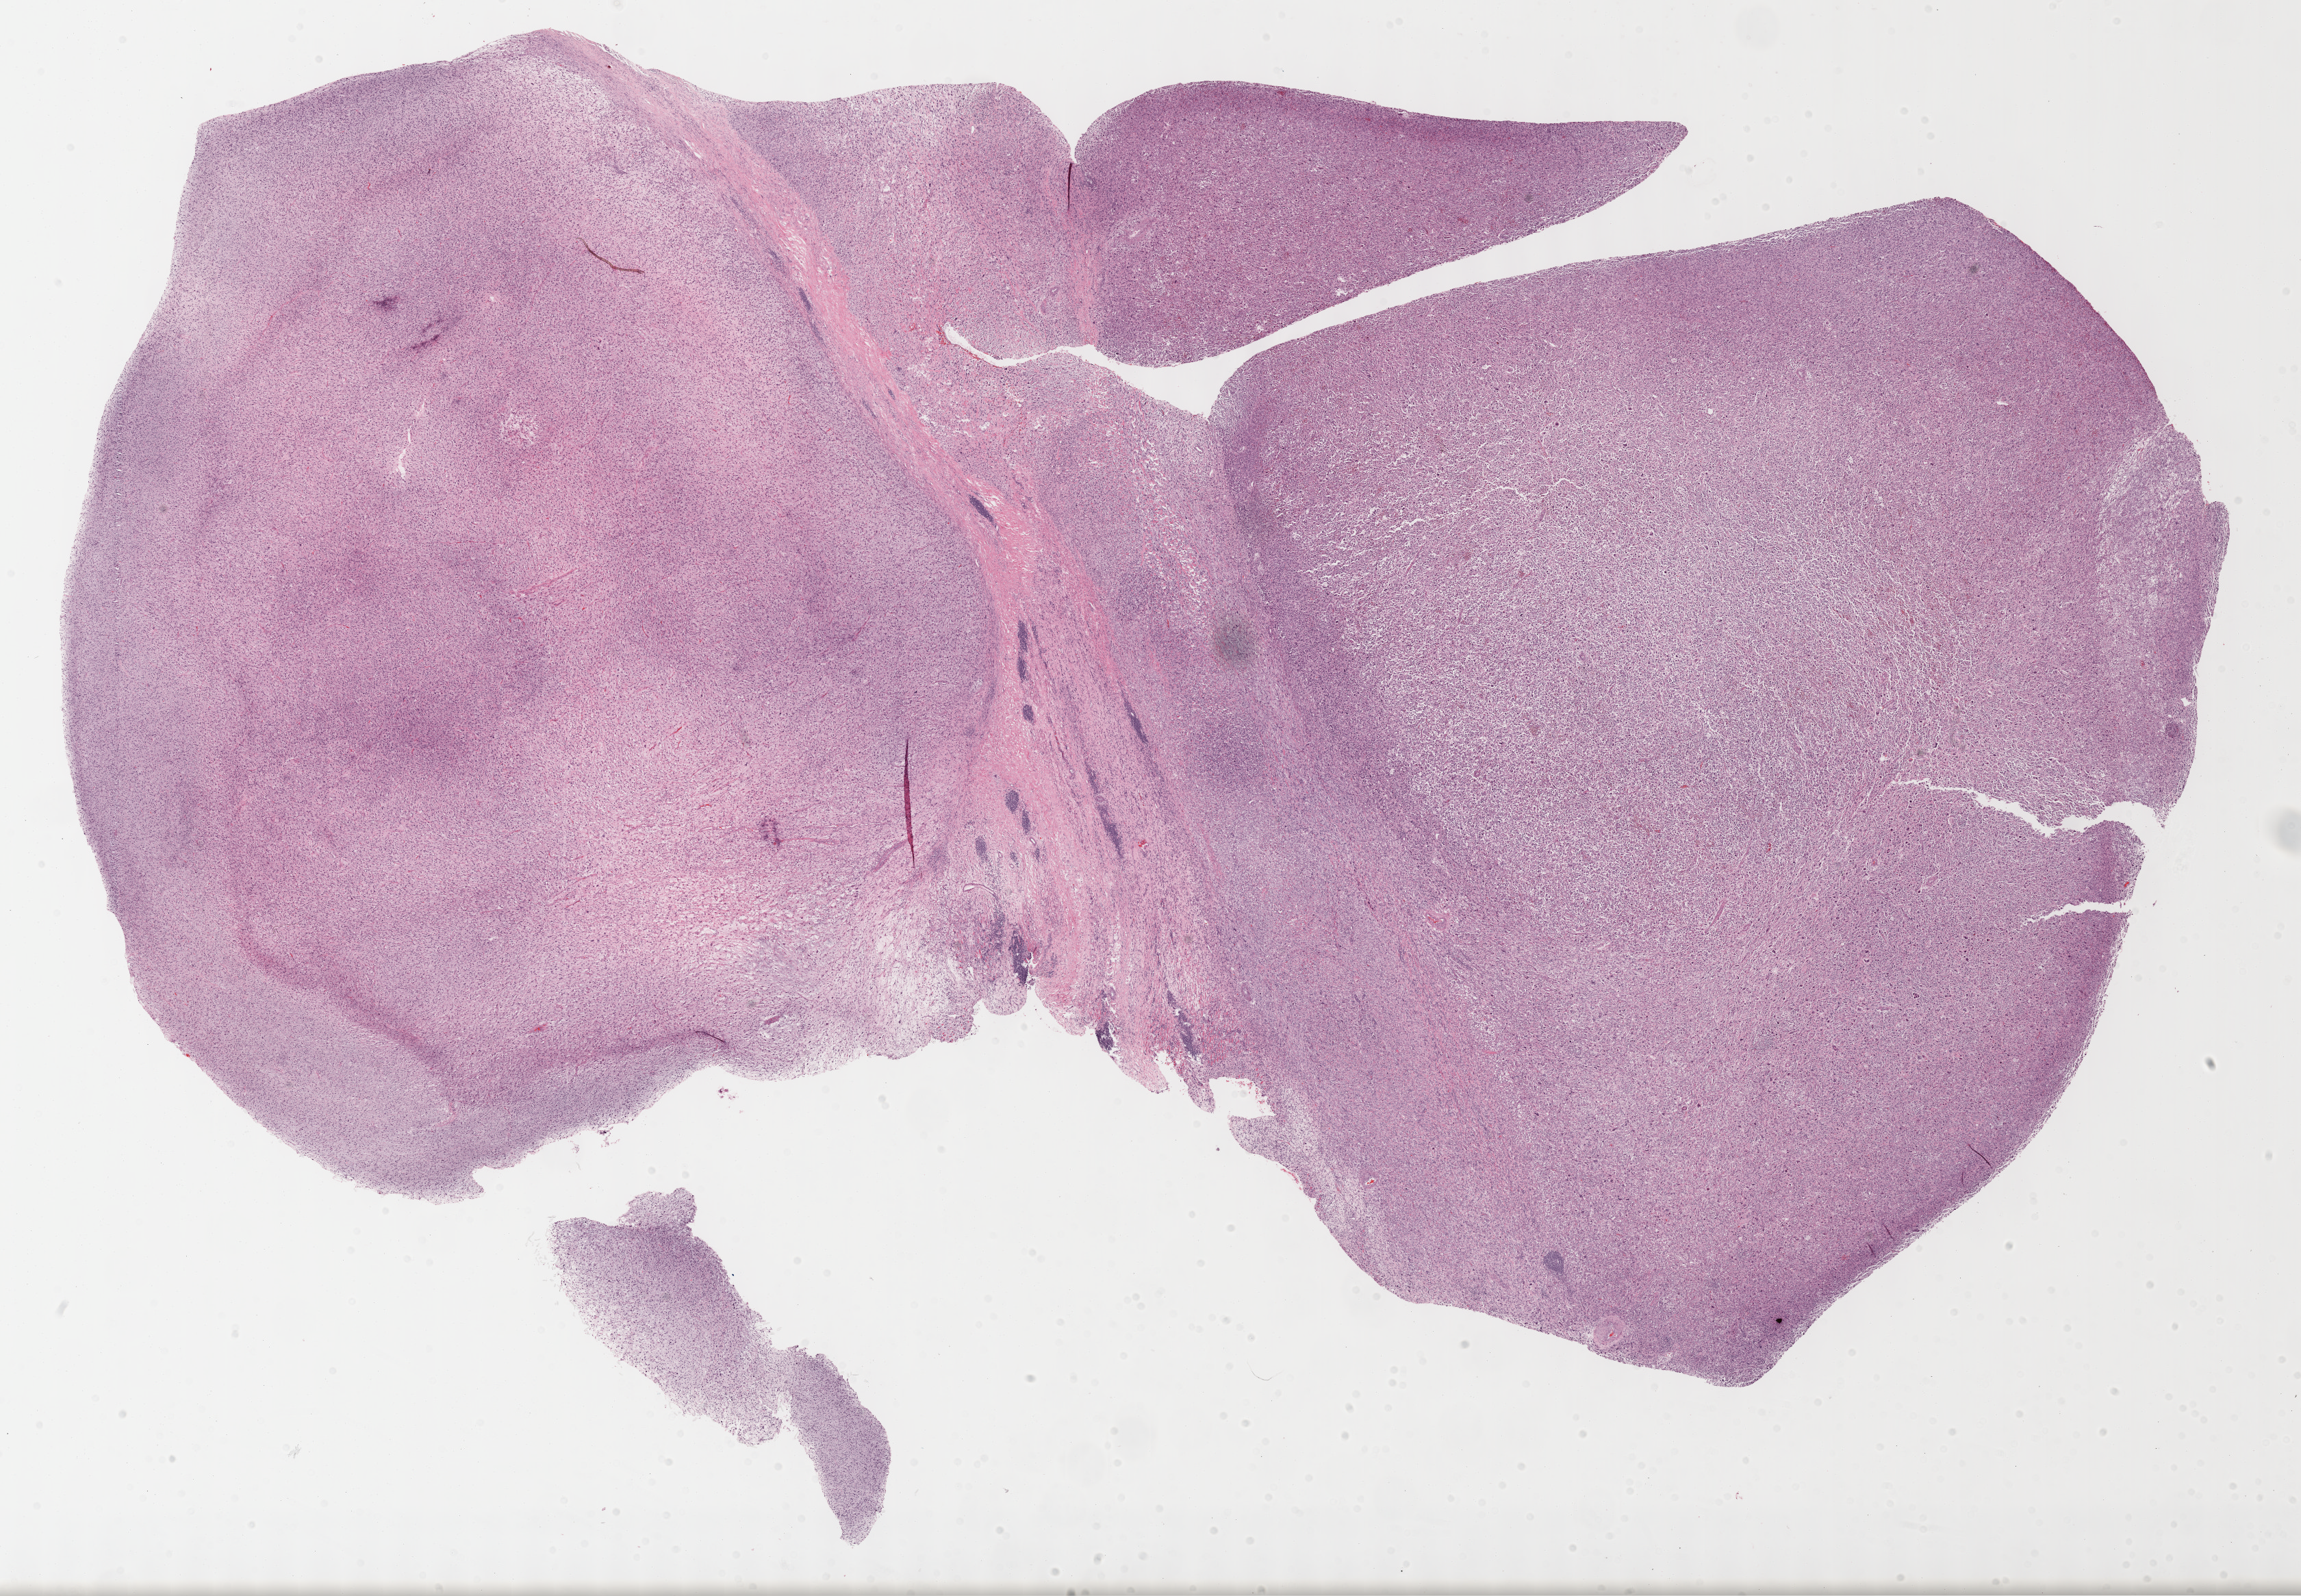
H&E whole-slide image, a low-resolution overview of the entire scanned area, about 27.2 x 18.9 mm (acquisition: 40x scan), FFPE section, primary tumour sample from the connective, subcutaneous and other soft tissues. Female, age 61 years at initial diagnosis.
Histologic diagnosis: Undifferentiated sarcoma (connective, subcutaneous and other soft tissues of lower limb and hip).